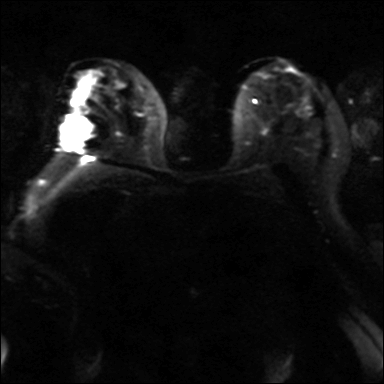
Breast MRI, one axial slice; position 21 of 42 along the scan axis; diffusion-weighted series; image 2 of 4 stored at this slice position (different b-values; order by instance number); 3 T; 384 × 384 image matrix, field of view 320 × 320 mm. Female patient.
Outlined on this slice (manually delineated by an expert):
- tumour on diffusion-weighted imaging: bounding box (x1, y1, x2, y2) in pixels: (64, 118, 92, 149)